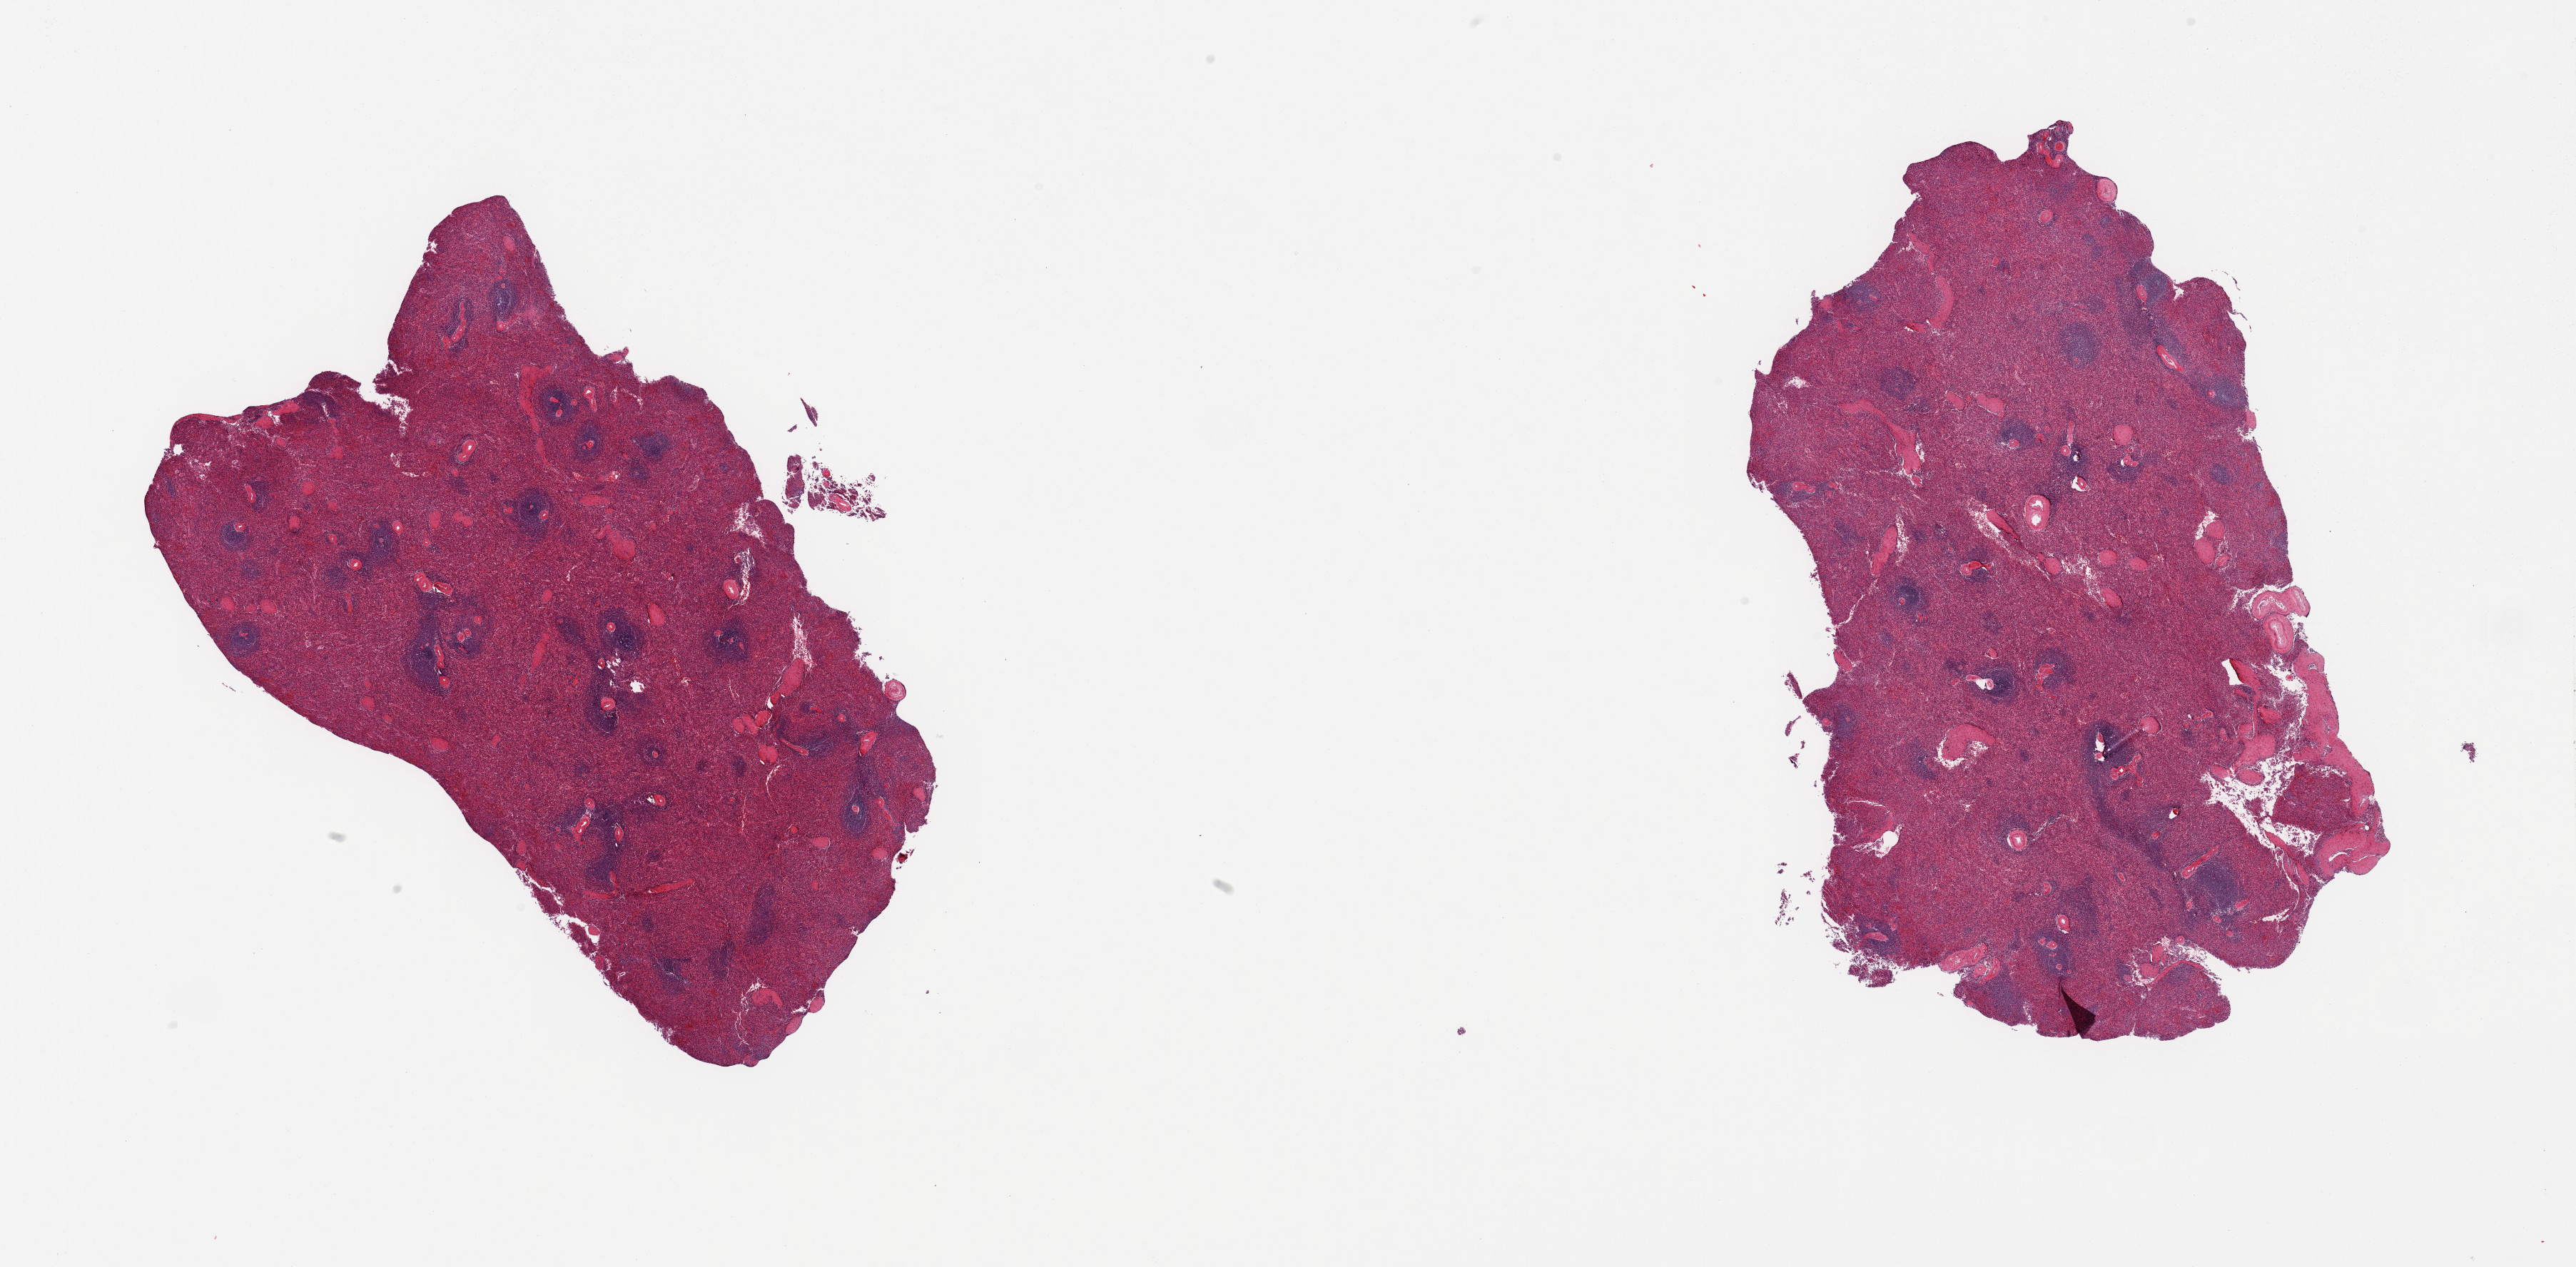
Whole-slide image, haematoxylin and eosin stain, brightfield — a low-resolution overview of the entire scanned area, about 28.5 x 14.0 mm (from a 20x scan), PAXgene-fixed paraffin-embedded (PFPE) section, section of spleen (target tissue), donor tissue sample. Donor: female.
Reviewer comment on this tissue sample: 2 pieces; slight congestion.